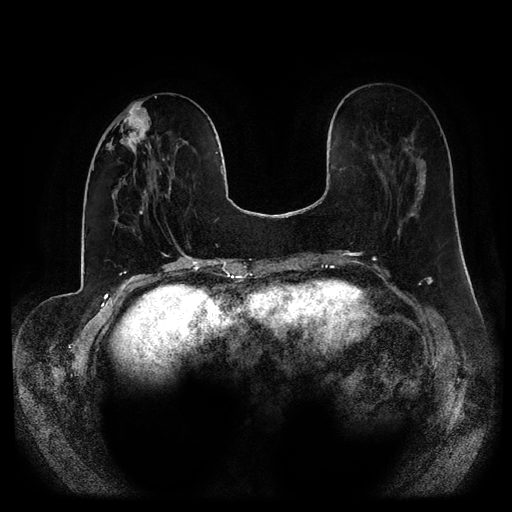
Breast MRI (dynamic contrast-enhanced, multi-phase), one axial slice; slice 33 of 116 in the series (ordered by position); dynamic contrast-enhanced series, time point 2 of 5 at this slice position (early post-contrast); 1.5 T; TE 2.6 ms, TR 5.2 ms; 512 × 512 image matrix, field of view 380 × 380 mm. Female patient, age 53 years.
Outlined on this slice (semi-automatic segmentation, software-assisted and operator-edited):
- breast lesion (labelled 'tumour' in the annotation; benign lesions carry a separate 'benign' label): bounding box (x1, y1, x2, y2) in pixels: (106, 101, 151, 153)